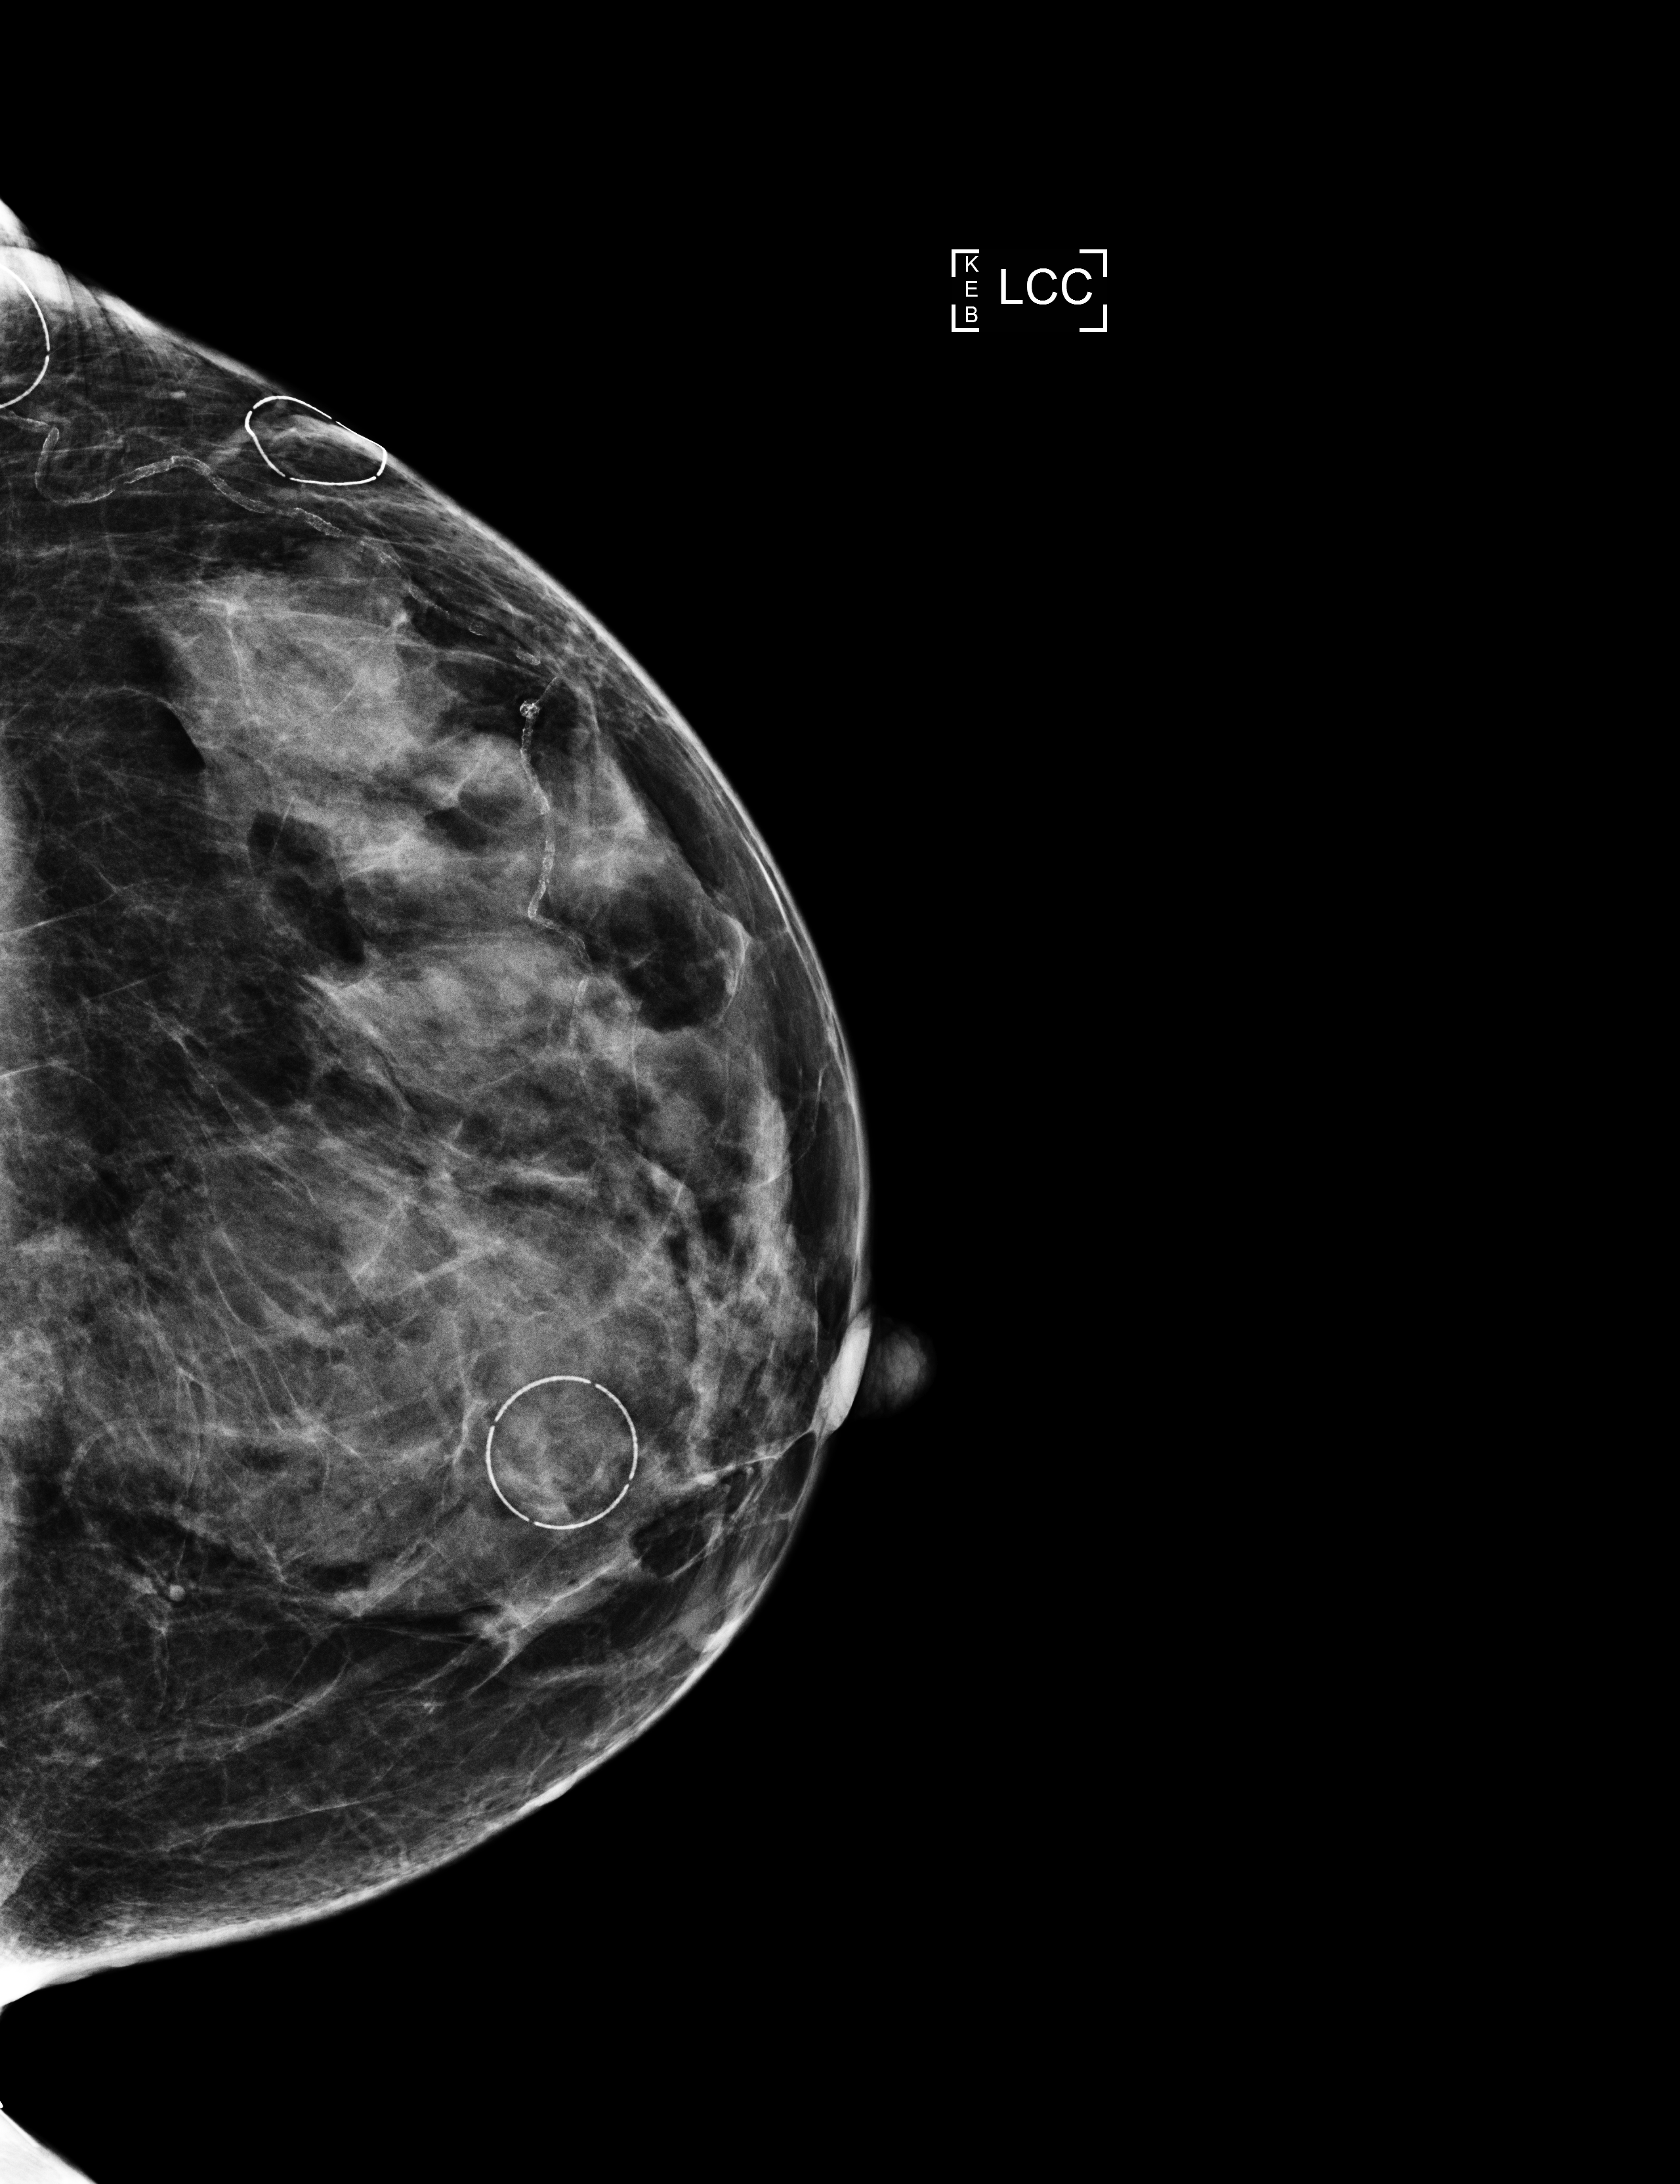
Screening examination, compressed breast thickness 38 mm. Patient aged 76 years (female).
Image type: full-field digital mammogram. Breast: left. Projection: CC view.